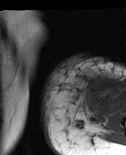
MRI of an extremity soft-tissue mass, one axial slice. Slice 18 of 86 in the series (ordered by position). MR volume resampled by the dataset authors to the PET/CT grid (not the native acquisition matrix). 3.27 mm slice thickness. 126 × 155 image matrix, field of view 123 × 151 mm. Female patient. Case-level facts recorded for this patient, not image findings: histological type: pleiomorphic leiomyosarcoma; grade: high; site of the primary tumour: left biceps.
Annotated regions visible in this slice (expert contour drawn on MRI and transferred to this co-registered scan by the dataset authors):
- gross tumour volume including surrounding oedema: bounding box (x1, y1, x2, y2) in pixels: (88, 81, 119, 110)
- gross tumour volume (mass): (93, 81, 105, 91)